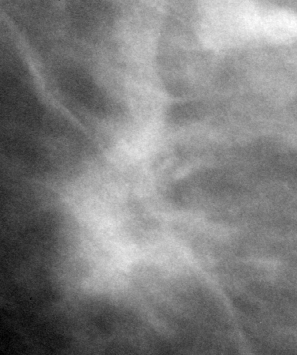
Region of interest cut from a scanned film mammogram (one marked finding); right breast; CC view.
Mass, shape irregular, margins spiculated; BI-RADS assessment category 3; subtlety rating 5 on a 1 (subtle) to 5 (obvious) scale; benign; no additional work-up was recommended (benign without callback).